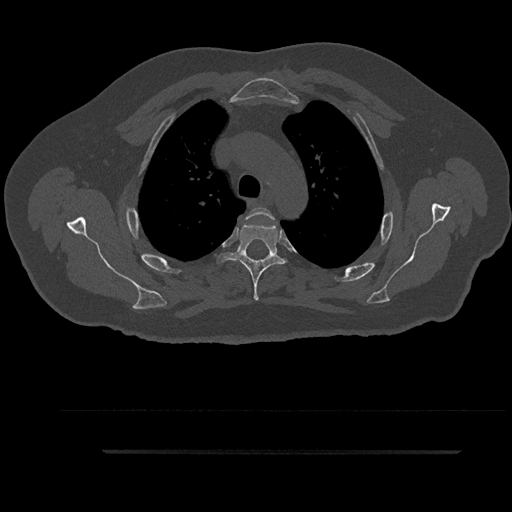
CT including the spine, one axial slice. Position 677 of 797 along the scan axis. Reconstruction kernel Br40s/3. Bone window (W 1800 / L 400 HU). 0.5 mm slice thickness. 512 × 512 image matrix. Male patient, age 63 years. Case-level facts recorded for this patient, not image findings: primary cancer: renal.
Annotated regions visible in this slice (semi-automatically segmented with operator editing):
- T3 vertebra: bounding box <245,207,275,261> (left, top, right, bottom; pixels)
- T4 vertebra: <216,222,285,301>